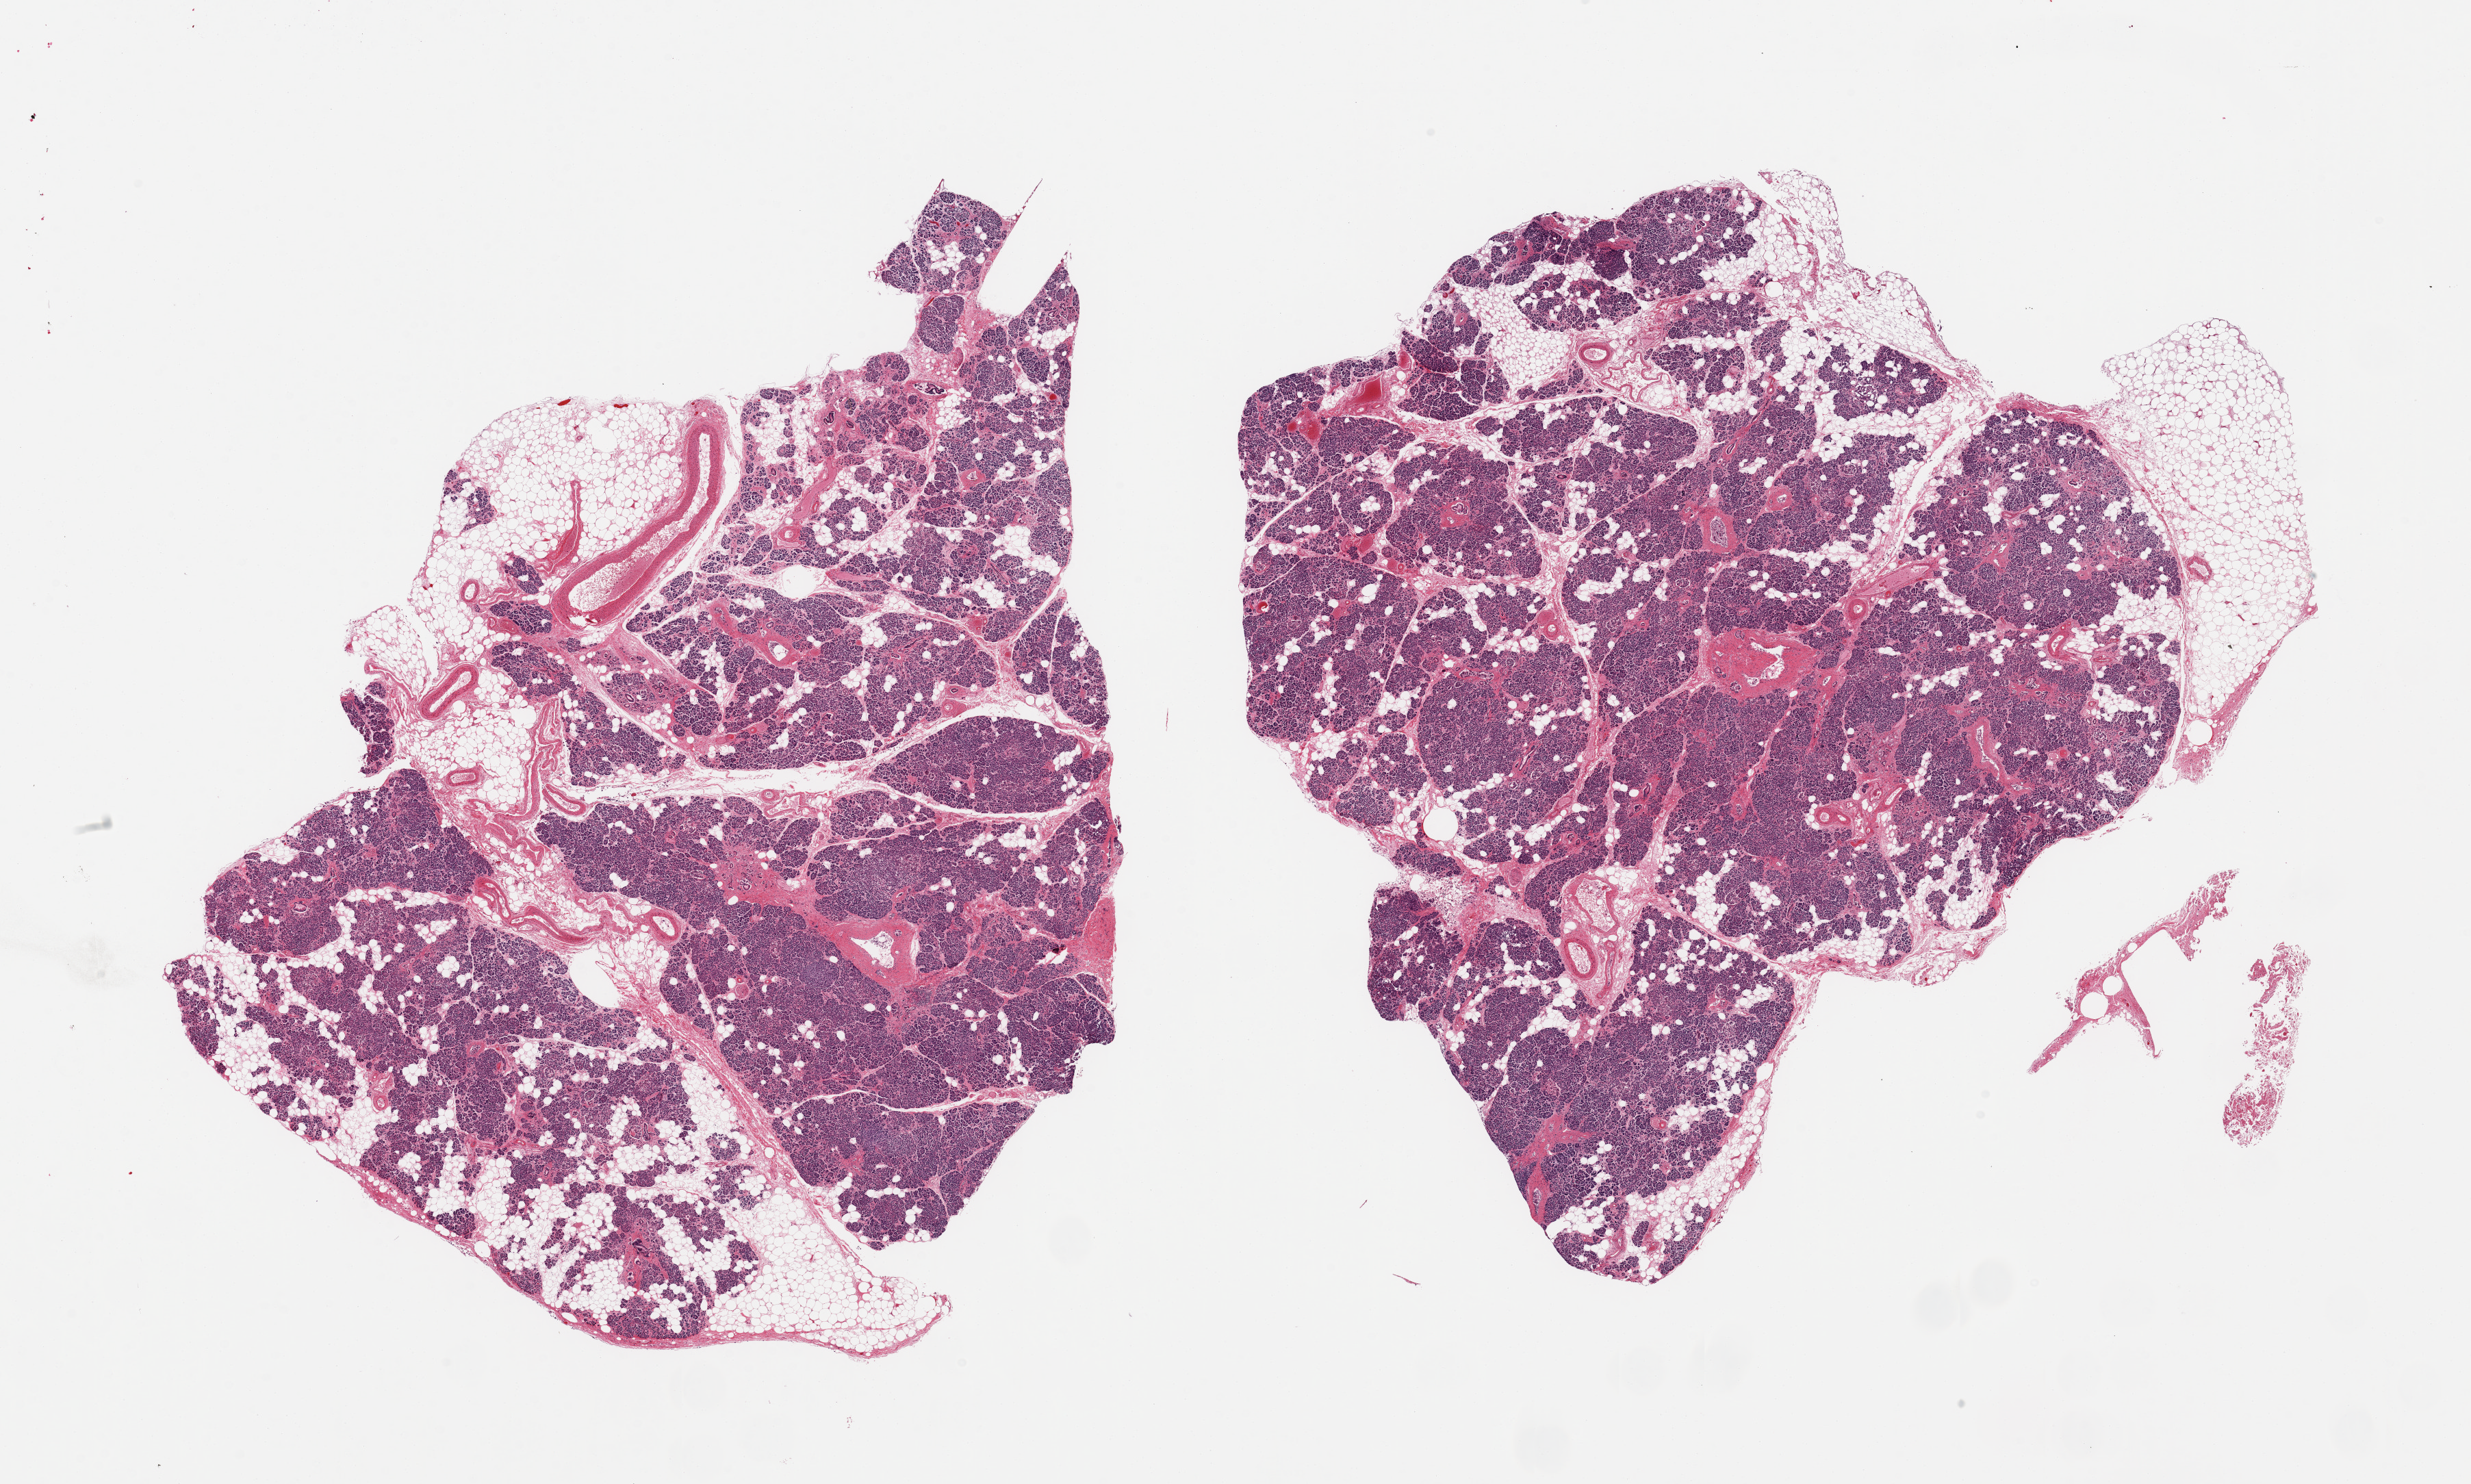
H&E whole-slide image, brightfield — low-resolution overview of the scanned area, about 28.5 x 17.1 mm. PAXgene-fixed, paraffin-embedded tissue. Sampled site (target tissue): pancreas. Tissue donor sample.
Pathologist's review note for this sample: 2 pieces, moderate saponification, Islets largely degraded, not well visualized.